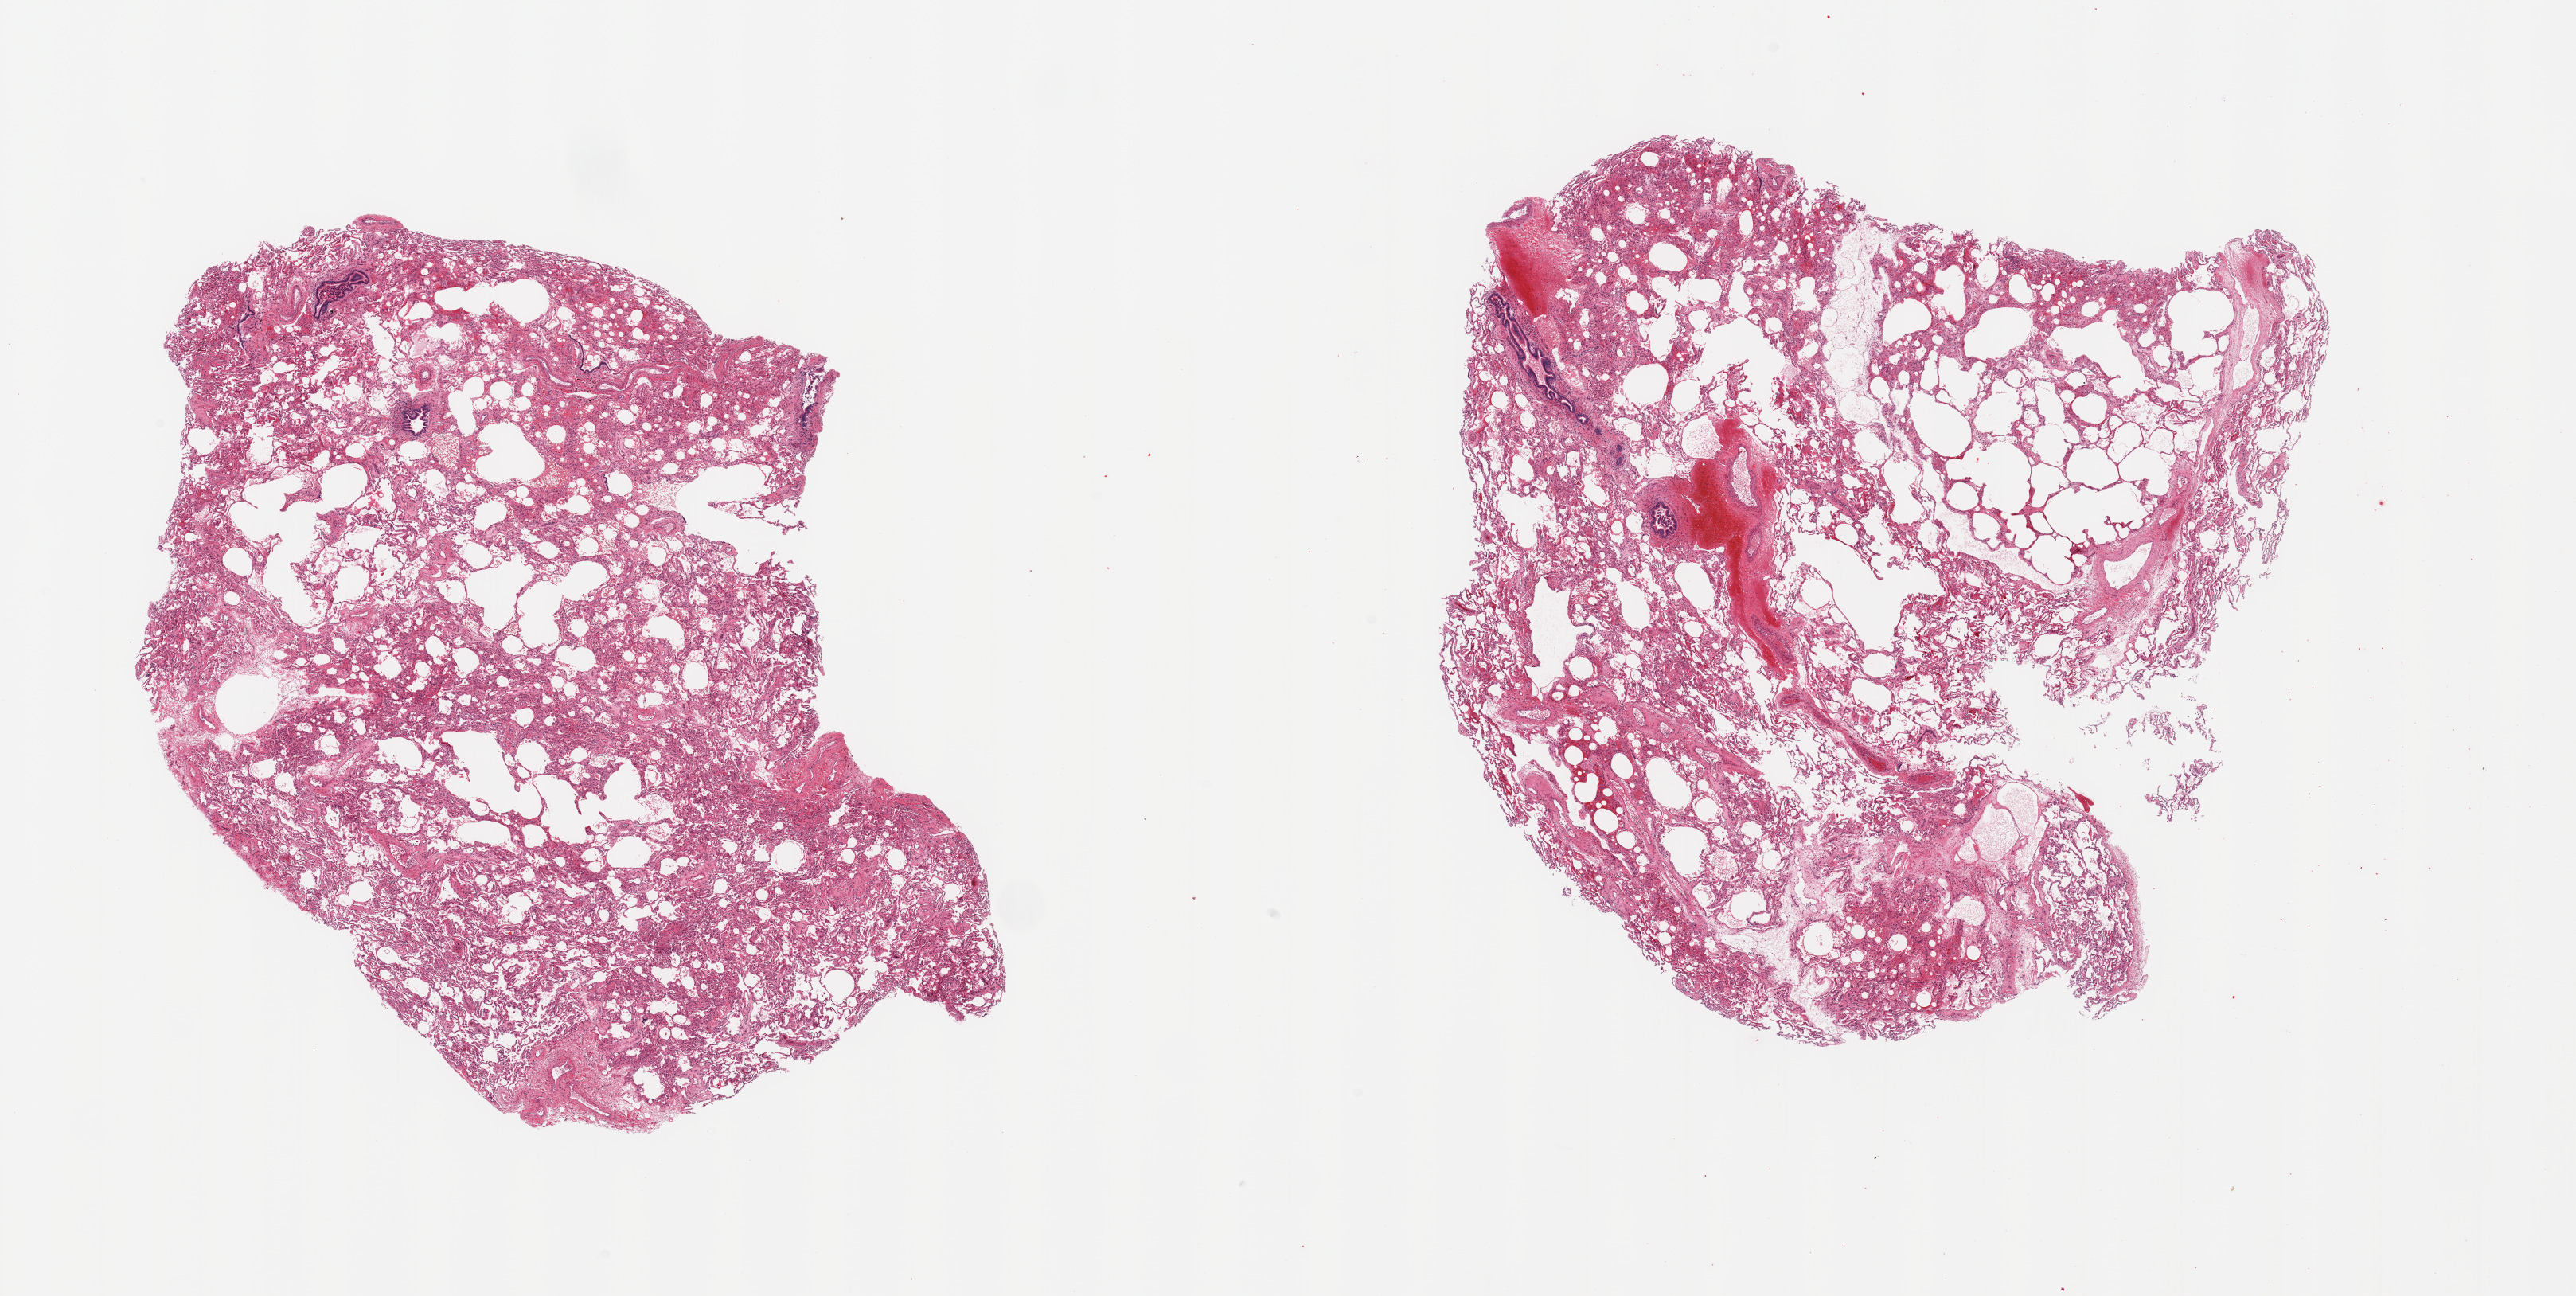
Whole-slide image, haematoxylin and eosin stain — shown as a low-resolution overview of the whole scanned area (about 25.6 x 12.9 mm), PAXgene-fixed, paraffin-embedded tissue, sampled site (target tissue): lung, tissue donor sample.
Reviewer comment on this tissue sample: 2 pieces; emphysema; focal vascular congestion & hemorrhage.